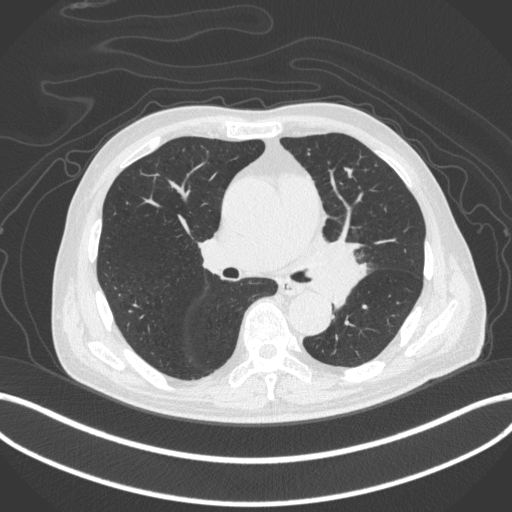
Chest CT, one axial slice. Slice 248 of 420 in the series (ordered by position). Reconstruction kernel B31f. Lung window (W 1500 / L -600 HU). 512 × 512 image matrix. Patient: male, 77 years. From the clinical record (not read from this slice): clinical TNM (as recorded): T3 N1 M0.
Structures marked on this image (bounding box drawn by a radiologist):
- lung tumour (recorded histology: adenocarcinoma): box from (x=303, y=230) to (x=371, y=303) px